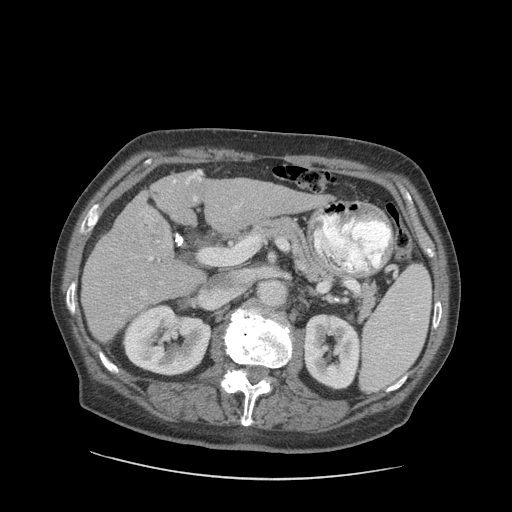
Contrast-enhanced abdominal CT (liver protocol), one axial slice; position 45 of 89 along the scan axis; reconstruction kernel STANDARD; 140 kVp; soft-tissue window (W 400 / L 40 HU); 512 × 512 image matrix. From the clinical record (not read from this slice): diagnosis: hepatocellular carcinoma (patient treated with transarterial chemoembolisation; whether this scan precedes or follows treatment is not stated here); TNM stage (as recorded): Stage-I; Child-Pugh class: A; tumour differentiation: moderately differentiated; tumour size: 4.6 cm.
Structures marked on this image (semi-automatically segmented with operator editing):
- liver parenchyma outside the tumour (the mass and vessels are separate outlines, so this box may not span the whole liver): bounding box [x1, y1, x2, y2] px = [80, 170, 326, 342]
- mass: [122, 207, 173, 256]
- liver vessels: [110, 171, 255, 313]